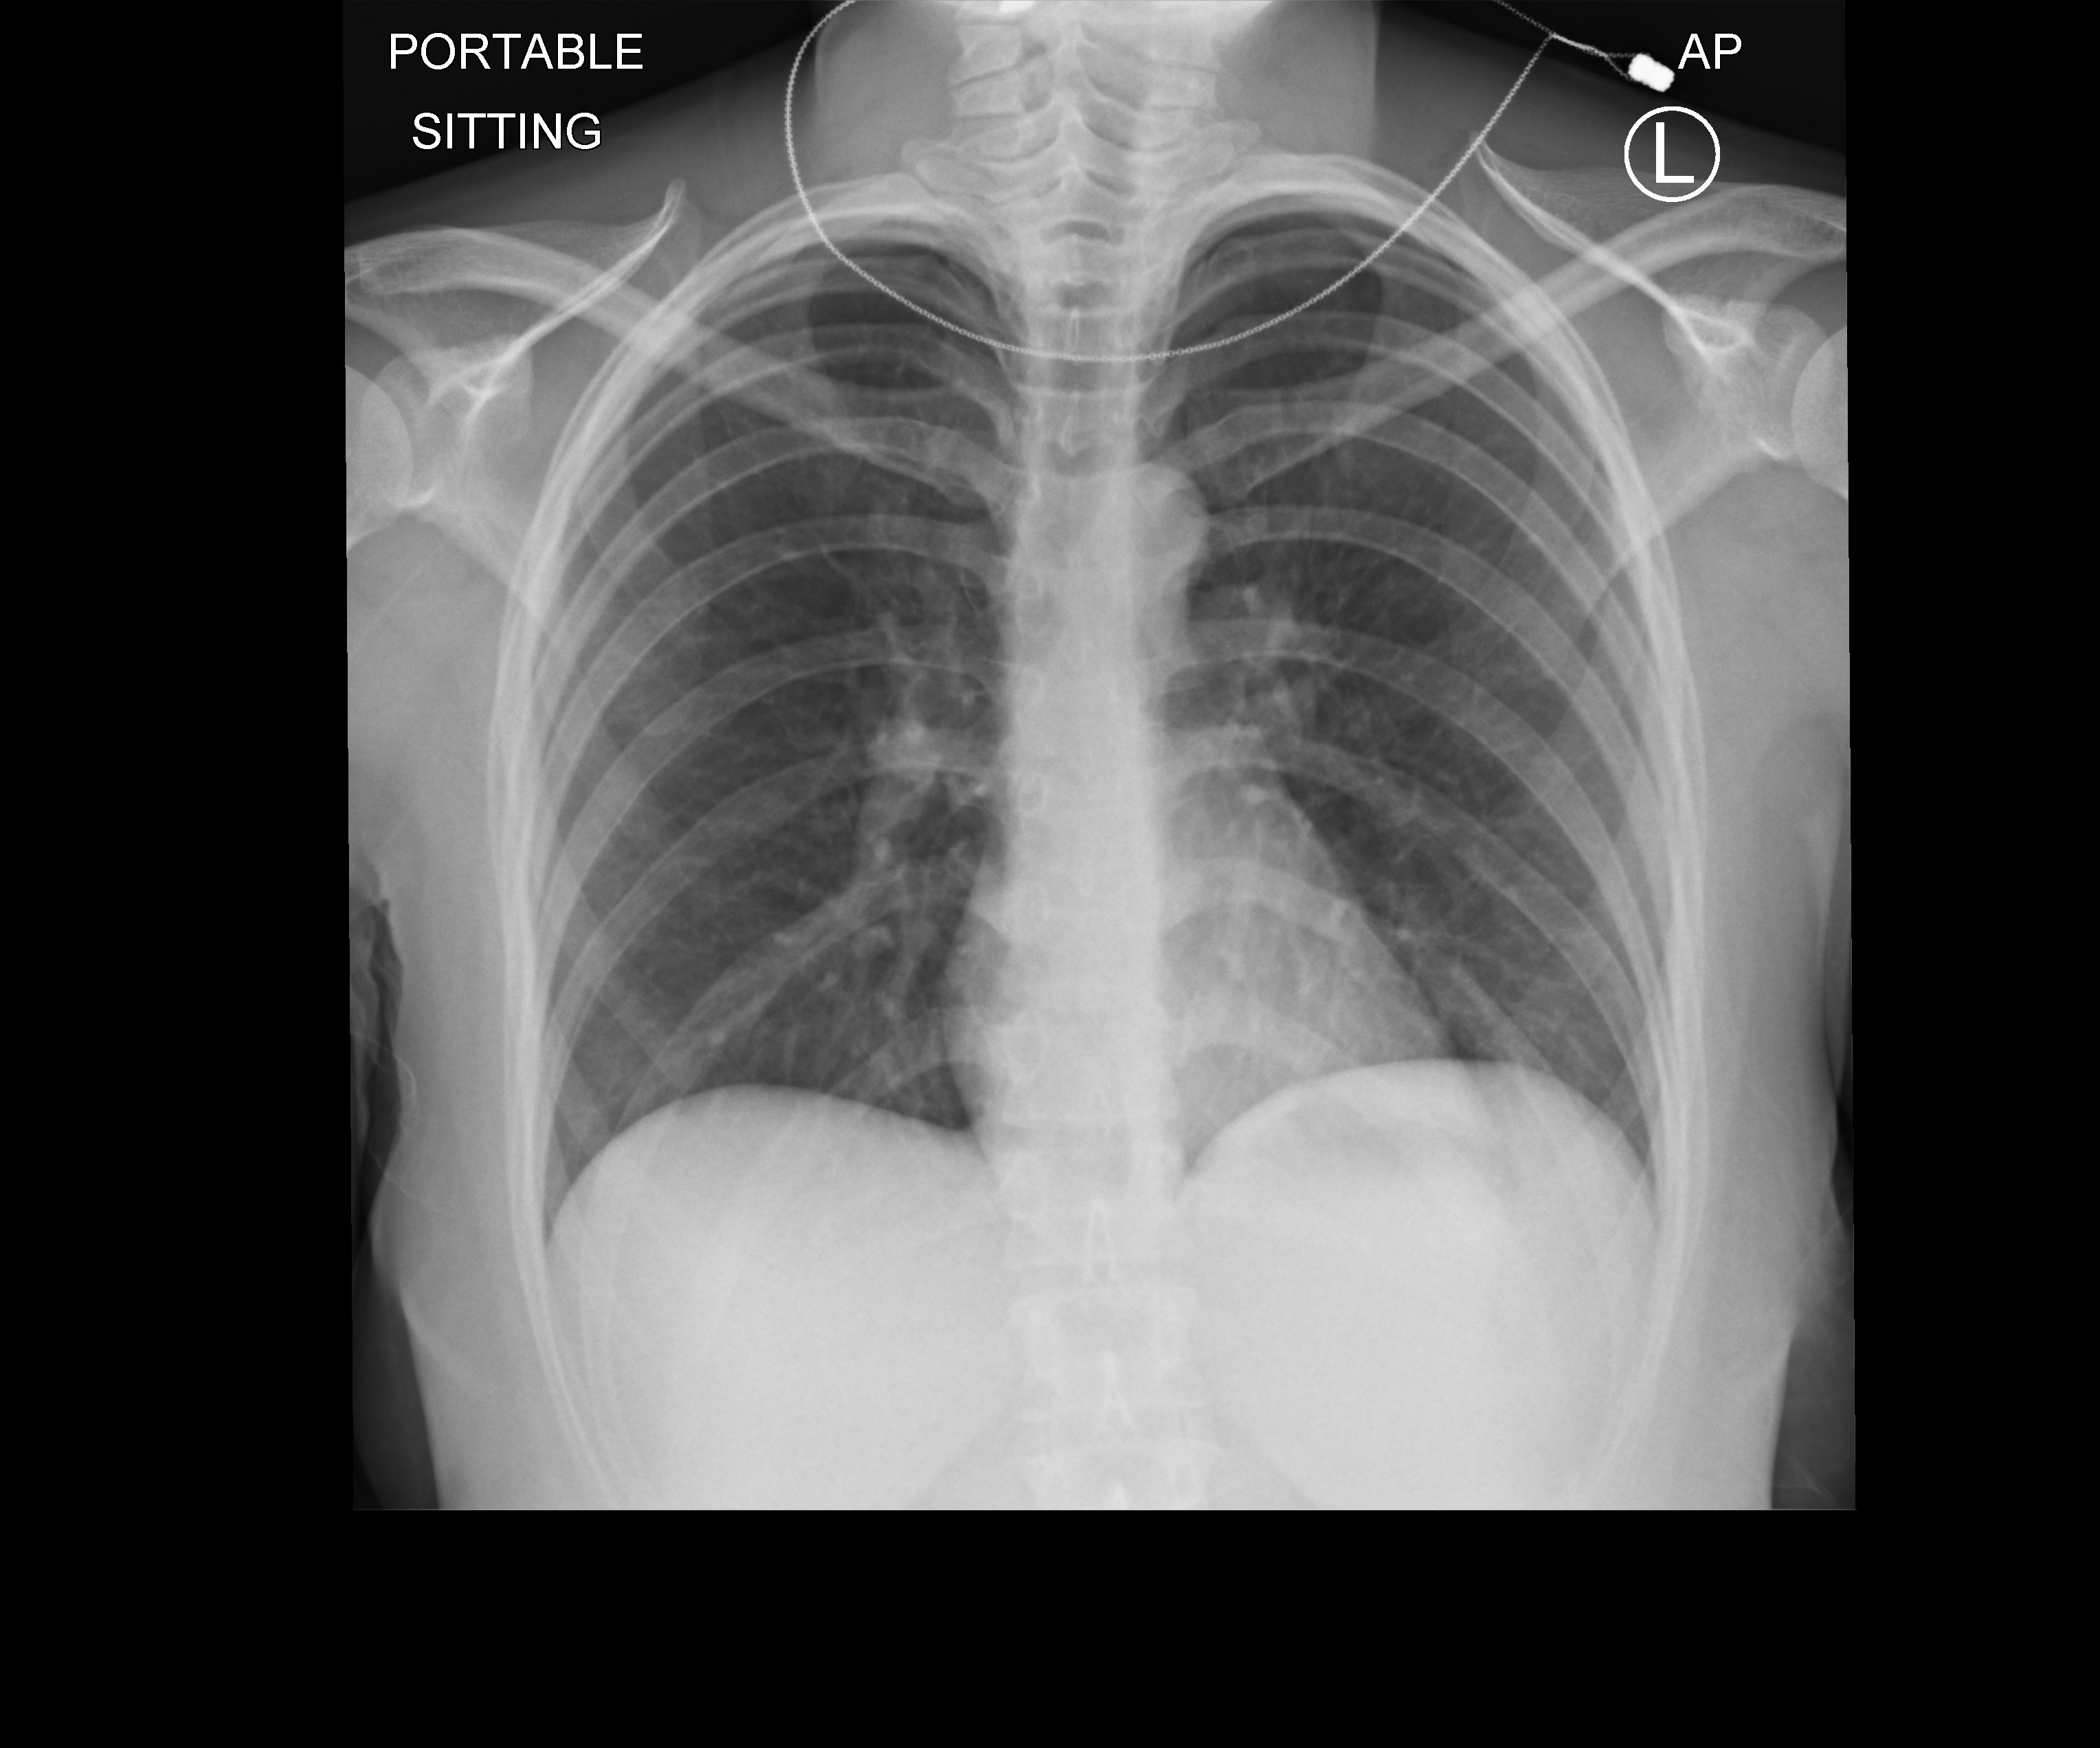
Bedside chest radiograph (computed radiography); anteroposterior (AP) projection. Patient hospitalised with COVID-19; female, aged 18–59 years.
Hospital-stay facts (about this admission, not read from this image; timing relative to this image not recorded):
- mechanically ventilated during this hospital stay: no
- admitted to intensive care during this hospital stay: no
- length of hospital stay: 1 day